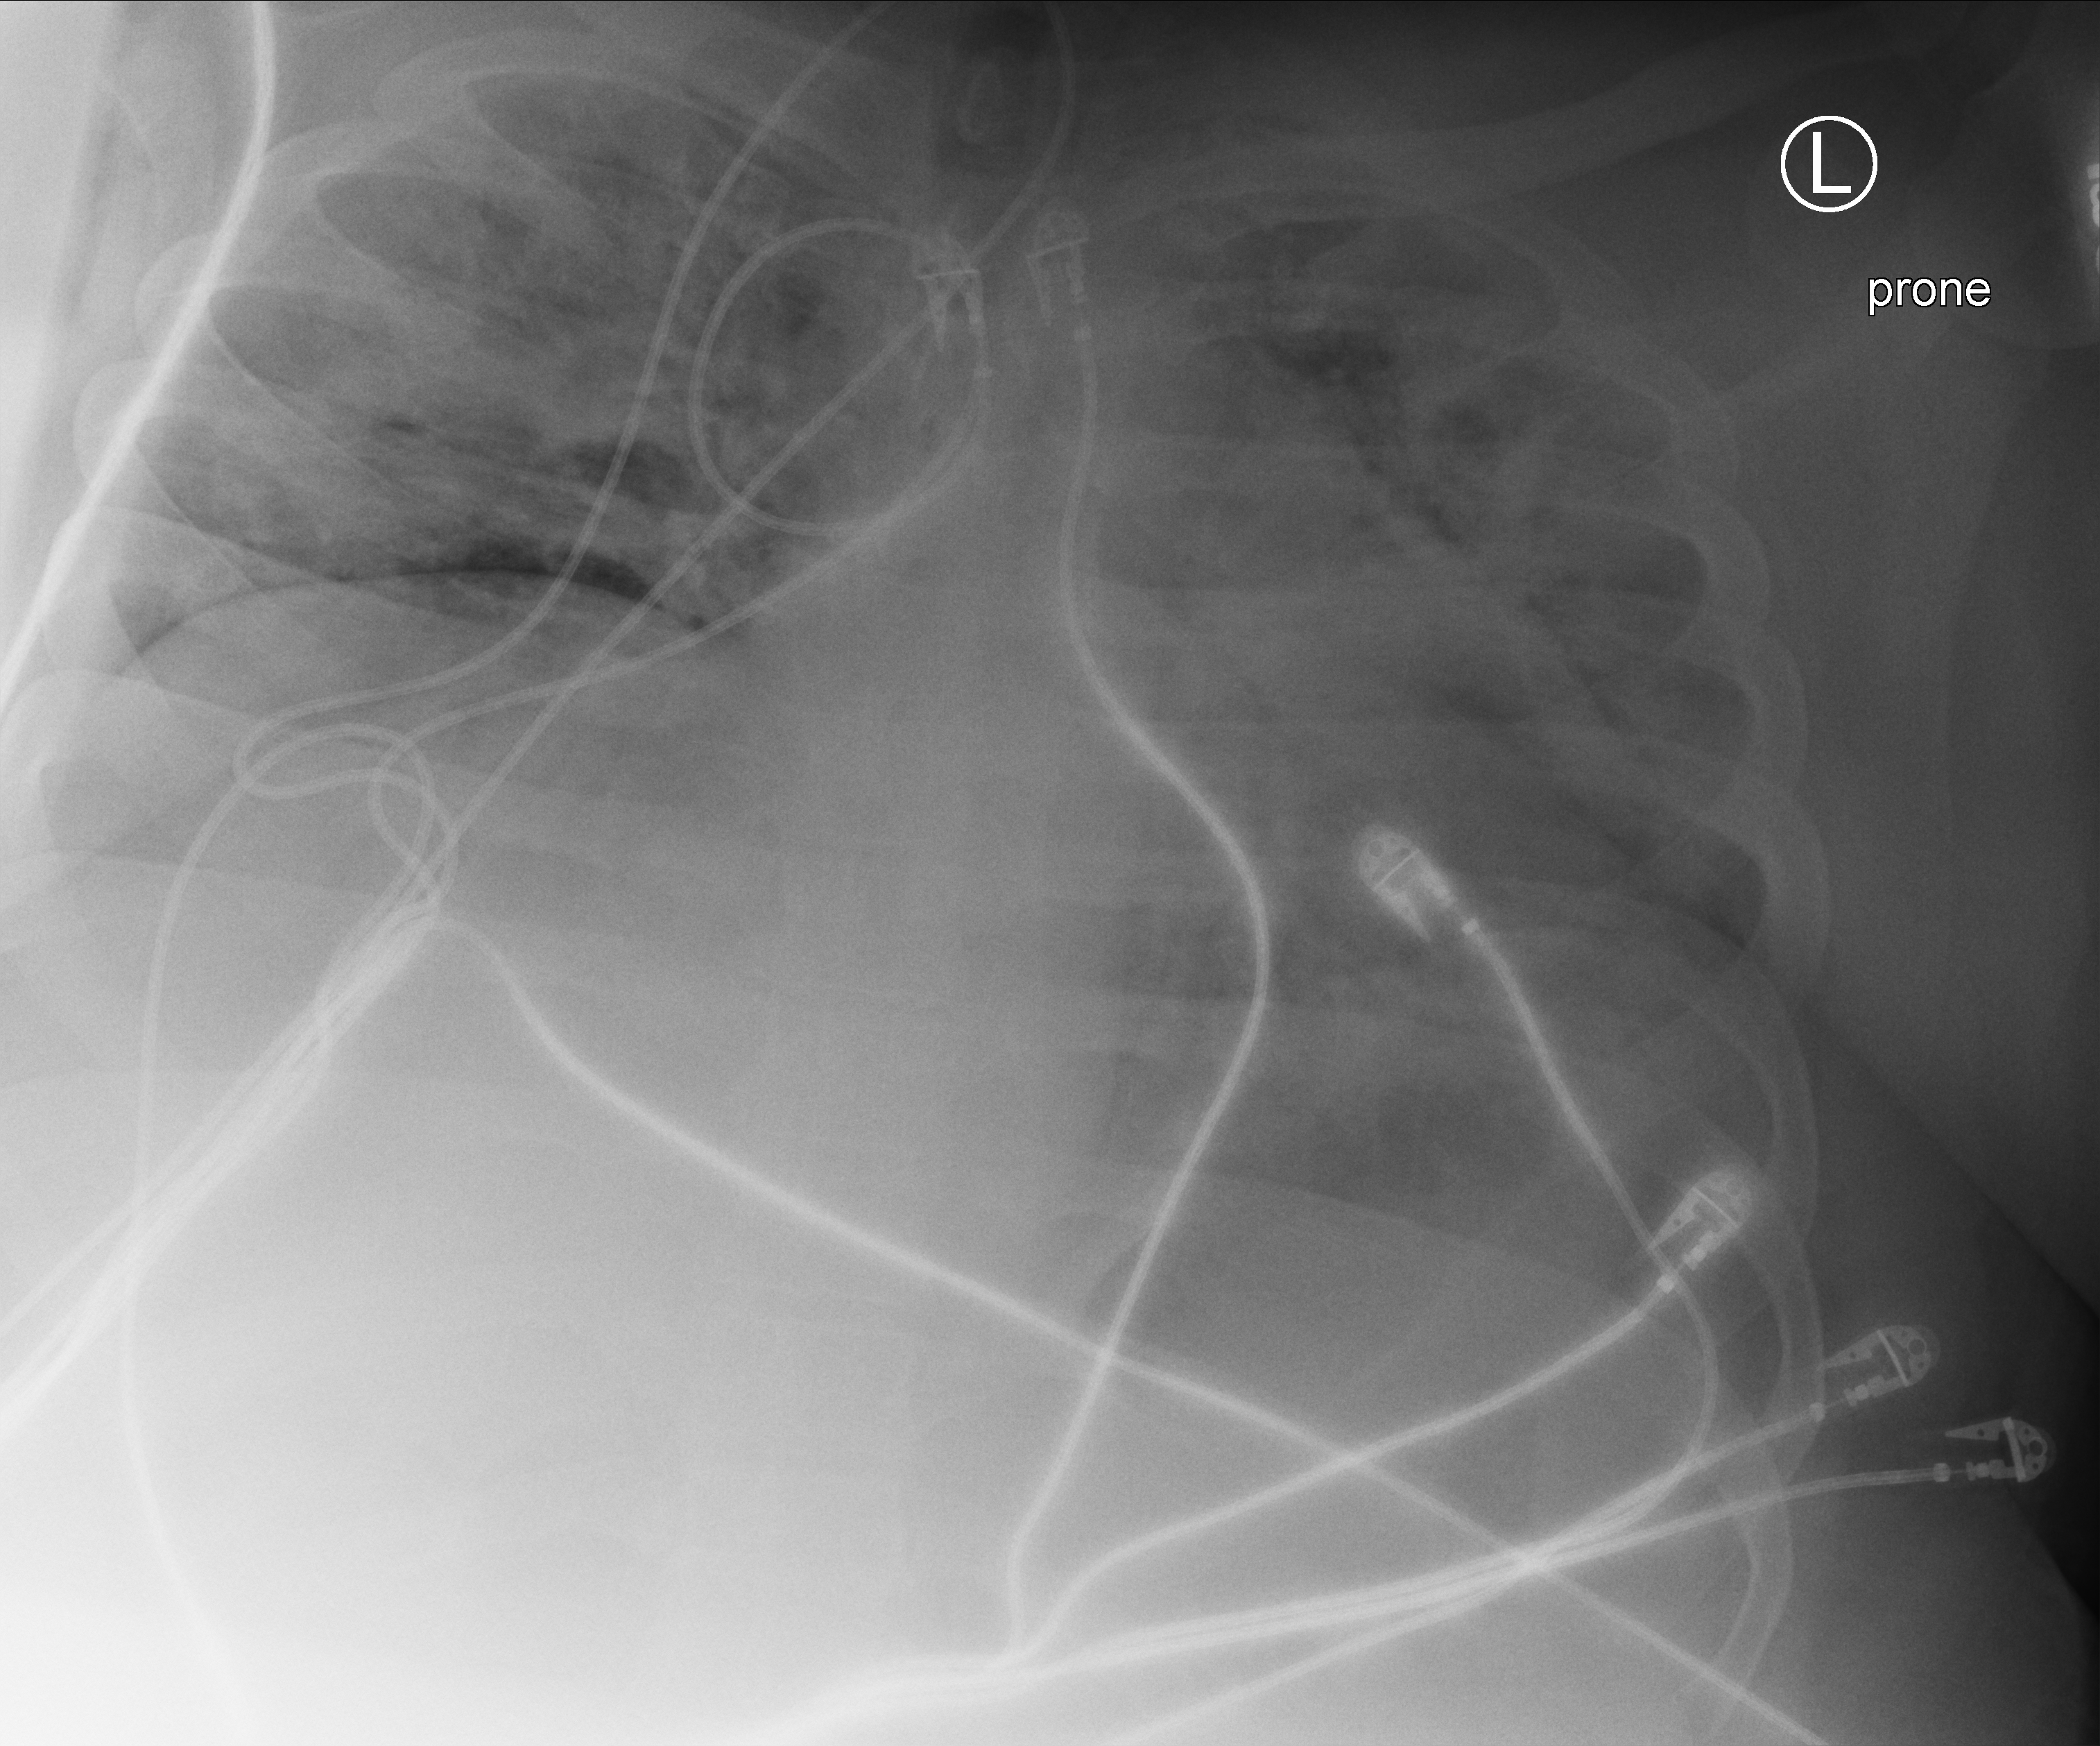
Portable chest radiograph. Male patient hospitalised with COVID-19, age 18–59 years.
Admission-level facts for this patient (not findings on this image; timing relative to this image not recorded):
- admitted to intensive care during this hospital stay: yes
- length of hospital stay: 69 days